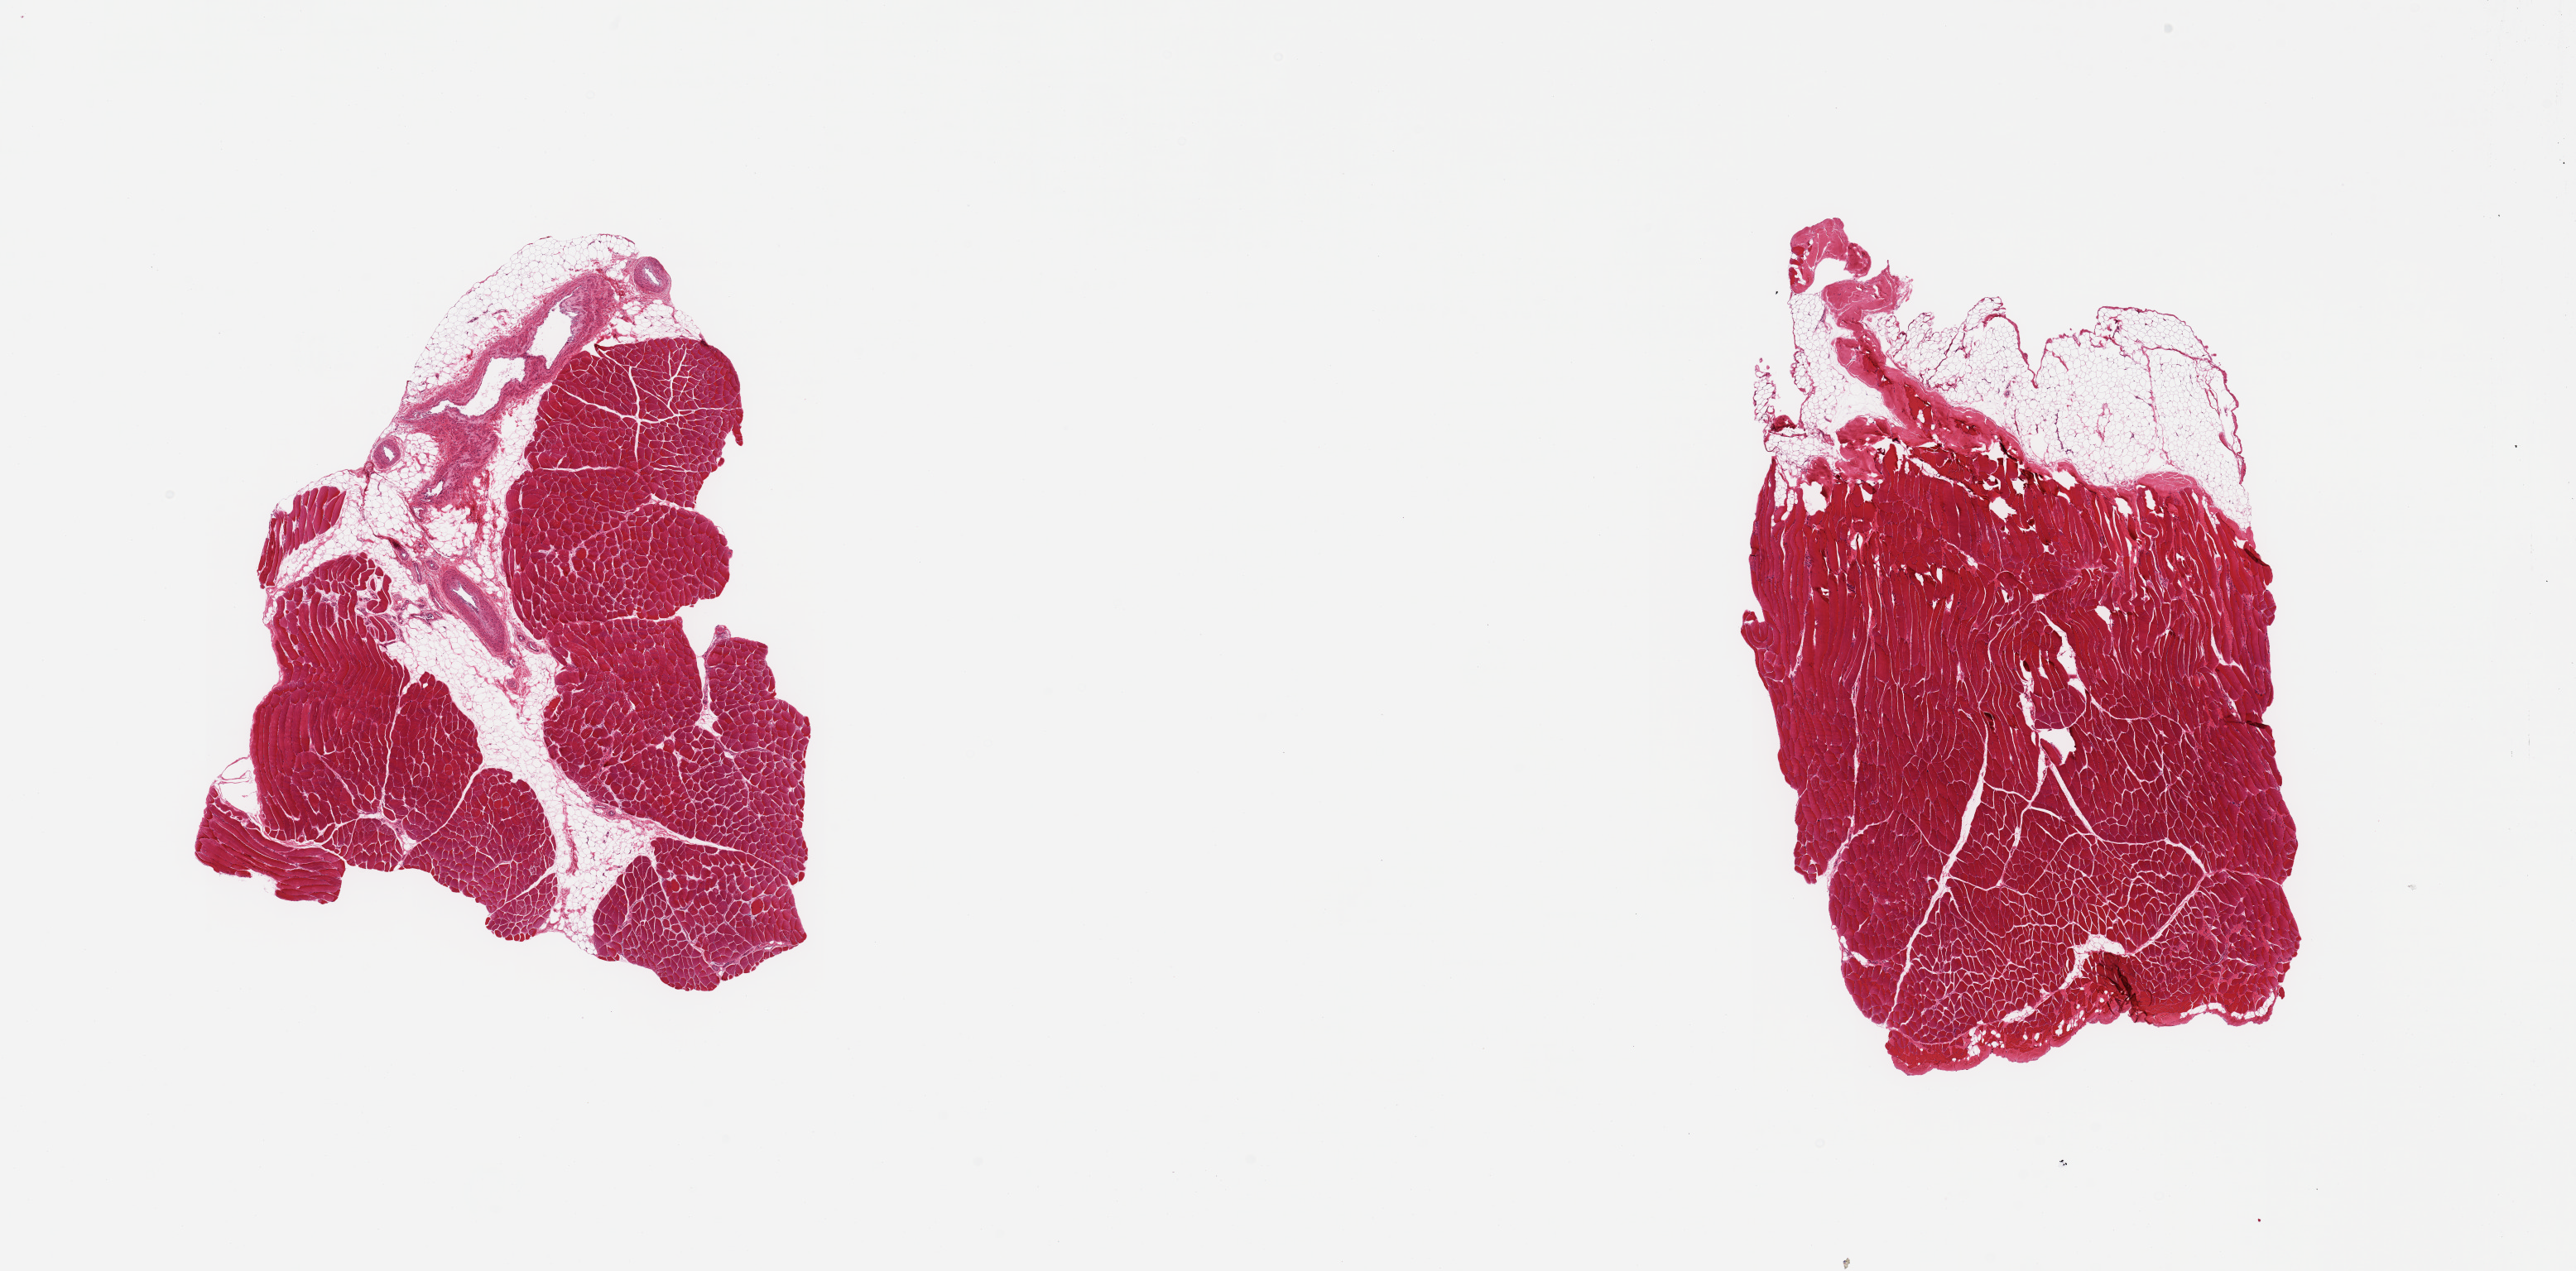
Whole-slide image, hematoxylin and eosin (H&E) stain, brightfield, whole scanned area (about 24.6 x 12.1 mm) shown as a low-resolution overview. PAXgene-fixed paraffin-embedded (PFPE) section. Target tissue: skeletal muscle. Donor tissue sample. Donor sex: female.
* review note (as recorded): 2 pieces; ~25% and 20% internal/external fat